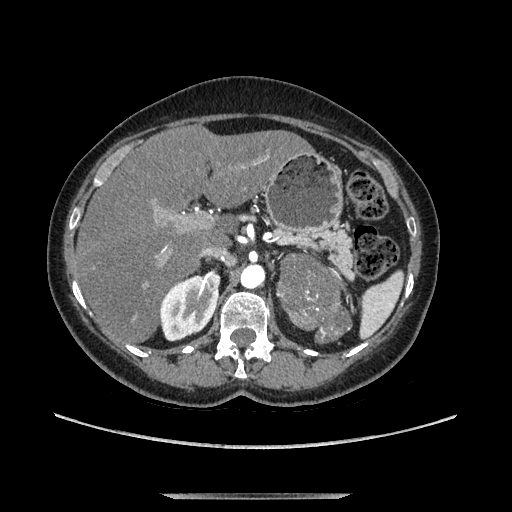
Contrast-enhanced abdominal CT, one axial slice. Soft-tissue window (W 400 / L 40 HU). 1.25 mm slice thickness. 512 × 512 image matrix, field of view 400 × 400 mm. Female patient. Case-level facts recorded for this patient, not image findings: diagnosis: adrenocortical carcinoma; tumour side: left adrenal; tumour size at pathology: 9 cm; Ki-67 index: 2 %; stage (as recorded): 3.
Structures marked on this image (semi-automatically segmented with operator editing):
- mass: bounding box (x1, y1, x2, y2) in pixels: (281, 258, 345, 343)